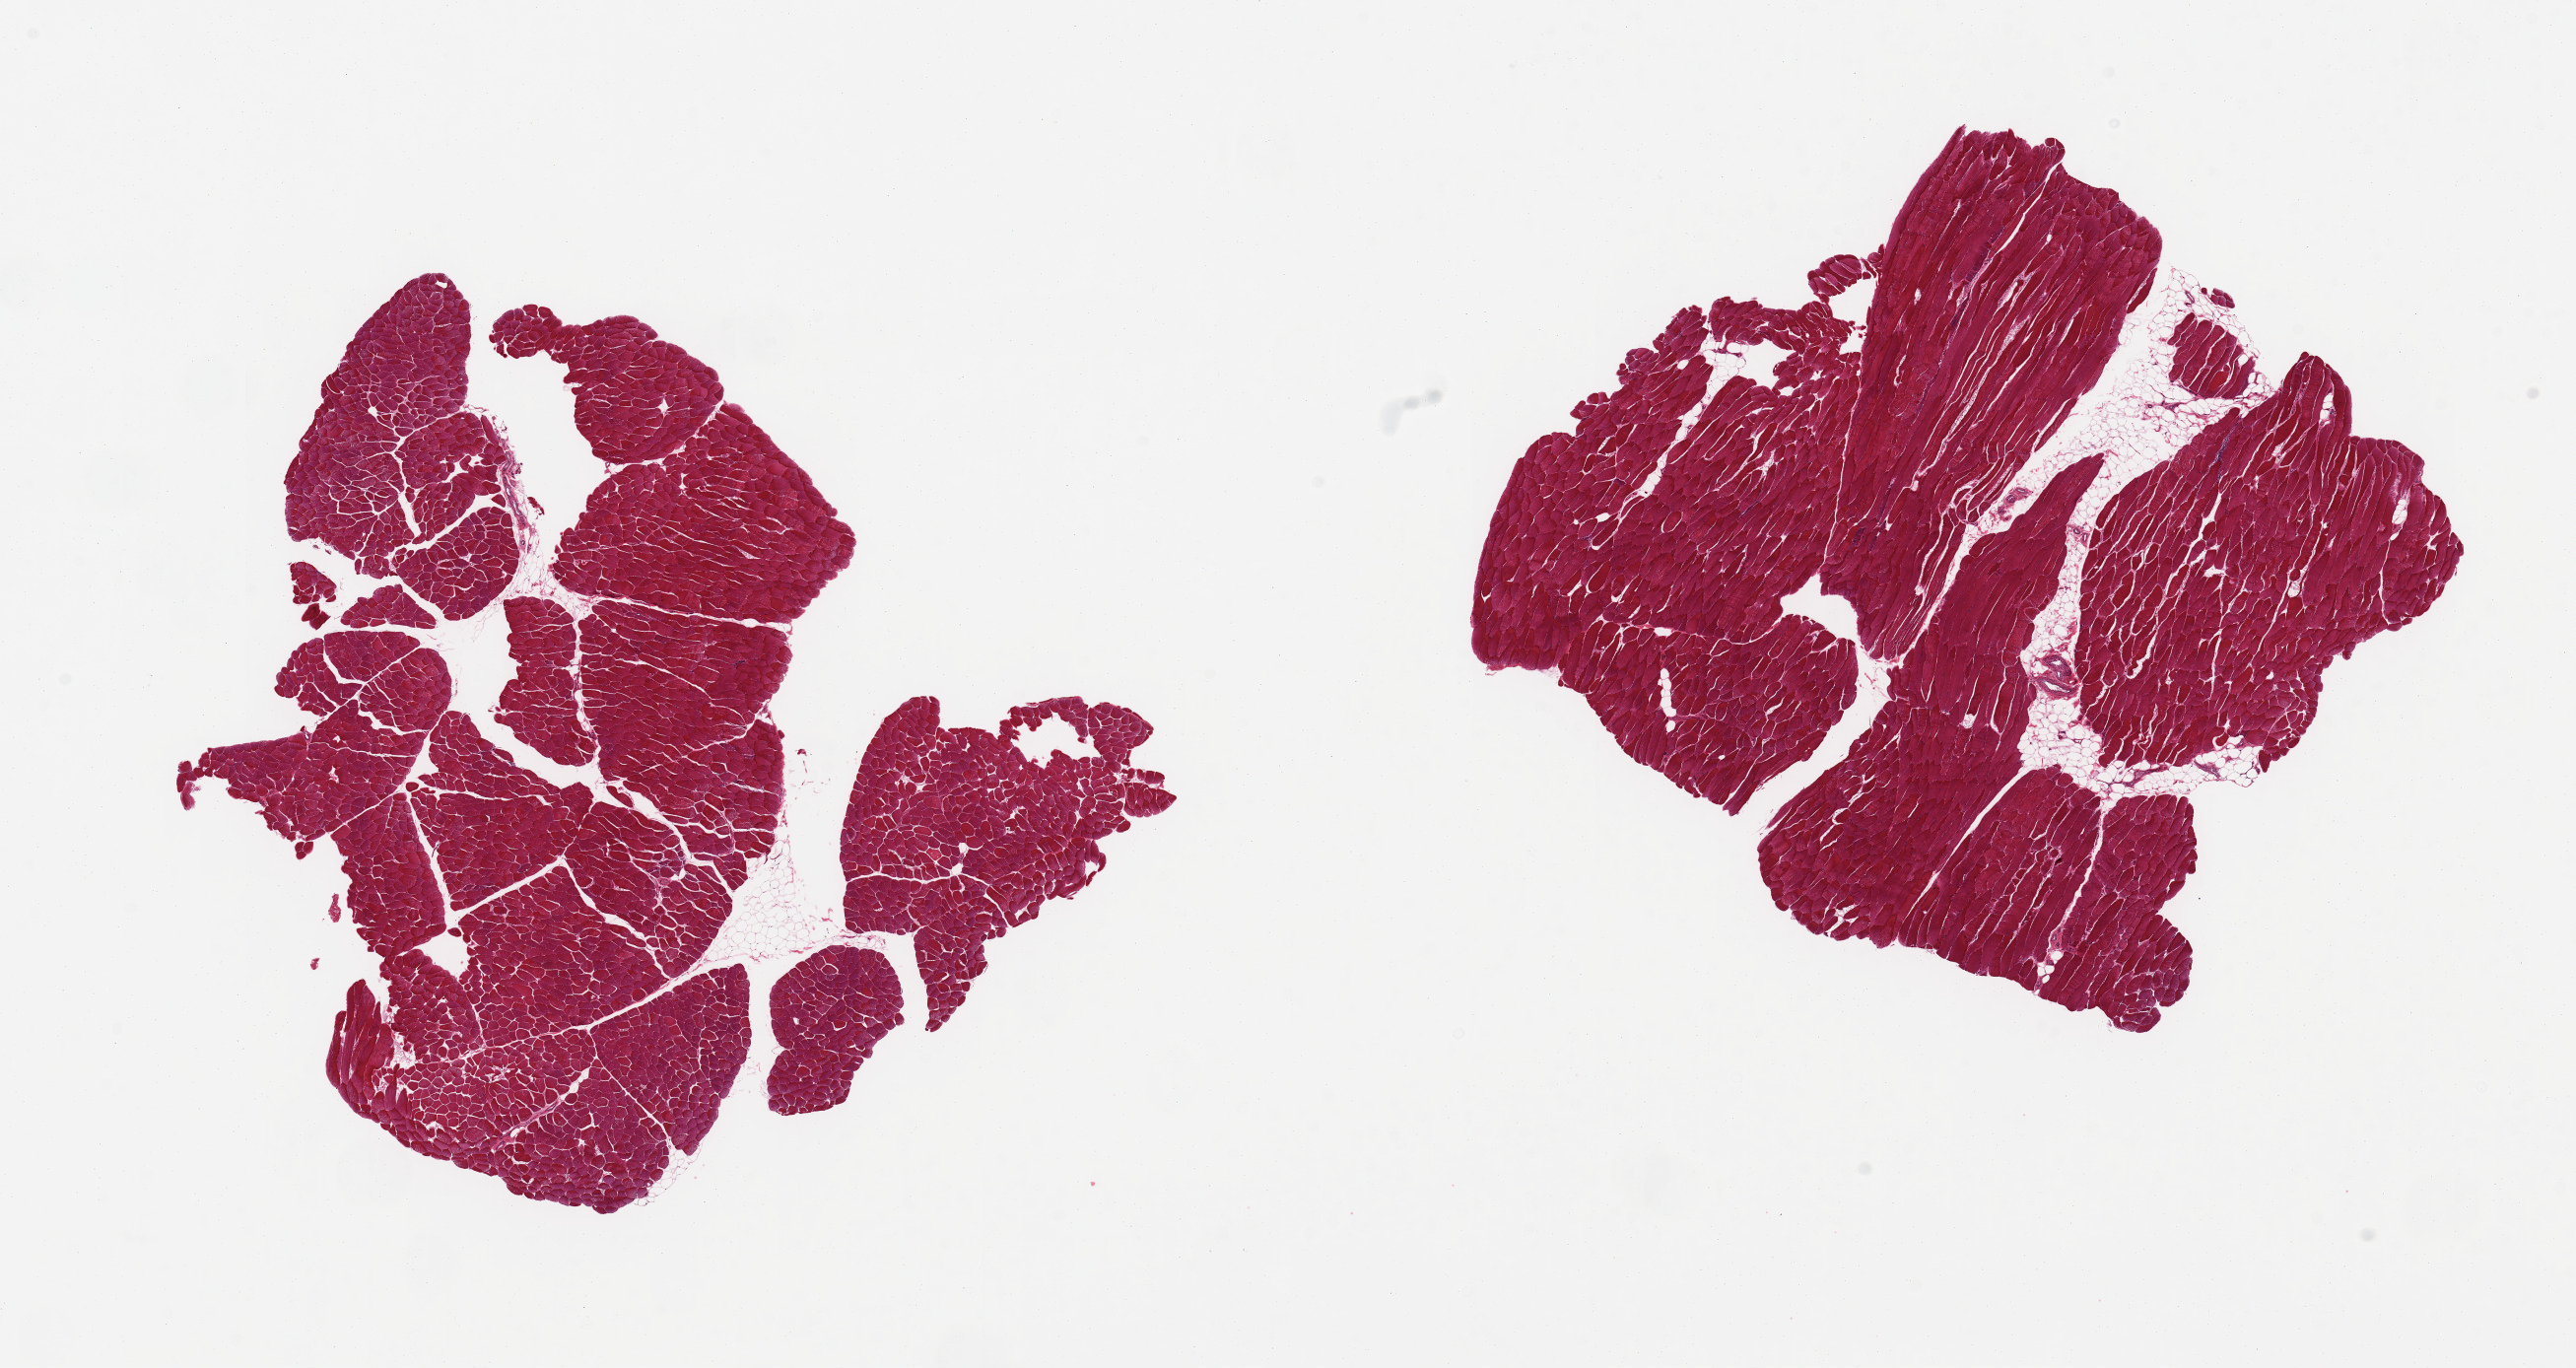
Digitized hematoxylin and eosin (H&E)-stained section, brightfield — a low-resolution overview of the entire scanned area, about 20.7 x 11.0 mm (acquisition: 20x scan); PAXgene-fixed paraffin-embedded (PFPE) section; sampled site (target tissue): skeletal muscle; donor tissue sample. Donor sex: male.
* reviewer comment on this tissue sample: 2 pieces; 5% internal fat